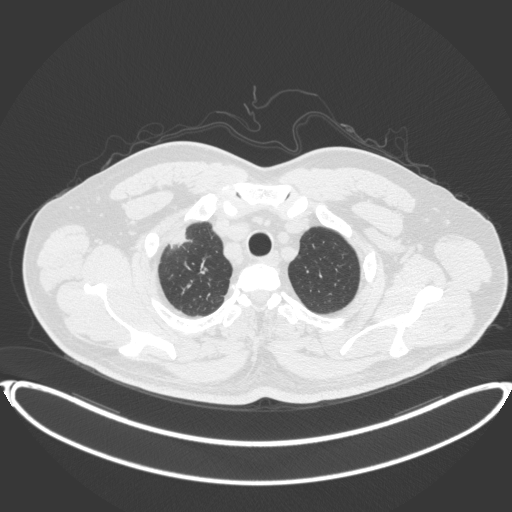
Chest CT, one axial slice. Slice 344 of 399 in the series (ordered by position). Reconstruction kernel B31f. 120 kVp. Lung window (W 1500 / L -600 HU). 512 × 512 image matrix, field of view 445 × 445 mm. Patient: male, 53 years. From the clinical record (not read from this slice): clinical TNM (as recorded): T2a N0 M0.
Annotated regions visible in this slice (rectangle marked by the reading radiologist):
- lung tumour (recorded histology: adenocarcinoma): box from (x=162, y=223) to (x=198, y=251) px